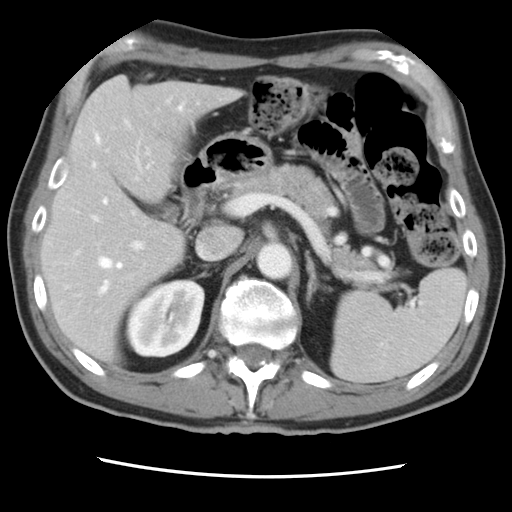
Contrast-enhanced abdominal CT, one axial slice. Slice 49 of 83 in the series (ordered by position). Intravenous contrast given. Soft-tissue window (W 400 / L 40 HU). 512 × 512 image matrix. Male patient, age 69 years. Case-level facts recorded for this patient, not image findings: diagnosis: colorectal cancer liver metastases, imaged before liver resection; multiple liver metastases: yes.
Outlined on this slice (expert manual segmentation):
- hepatic veins: bounding box <93,106,183,293> (left, top, right, bottom; pixels)
- liver: <44,76,237,360>
- planned liver remnant (the part of the liver to remain after resection): <43,136,186,360>
- portal vein (with intrahepatic branches): <75,215,144,255>